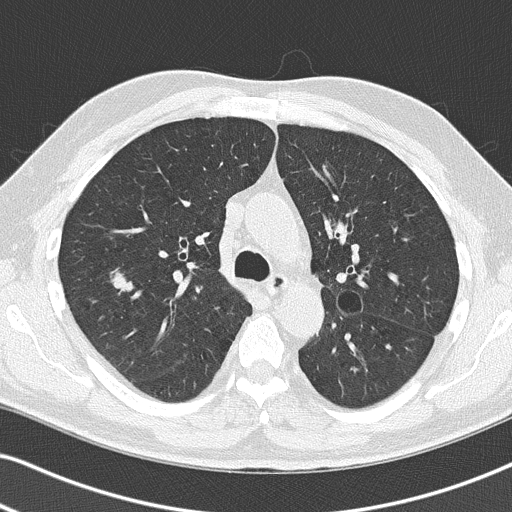
Low-dose screening chest CT, one axial slice. Position 89 of 140 along the scan axis. Reconstruction kernel B50f. 120 kVp. Lung window (W 1500 / L -600 HU). 2 mm slice thickness. 512 × 512 image matrix, field of view 330 × 330 mm.
Annotated regions visible in this slice (expert manual segmentation):
- lesion 1 (tumor, upper lobe of right lung): bounding box [x1, y1, x2, y2] px = [111, 271, 133, 291]